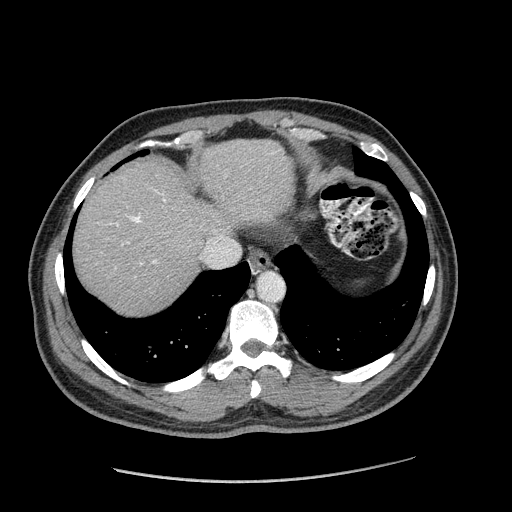
Contrast-enhanced abdominal CT (liver protocol), one axial slice. Slice 153 of 182 in the series (ordered by position). 120 kVp. Soft-tissue window (W 400 / L 40 HU). 512 × 512 image matrix. From the clinical record (not read from this slice): diagnosis: hepatocellular carcinoma (patient treated with transarterial chemoembolisation; whether this scan precedes or follows treatment is not stated here); TNM stage (as recorded): Stage-I.
Structures marked on this image (semi-automatic segmentation, software-assisted and operator-edited):
- abdominal aorta: bounding box <258,273,284,302> (left, top, right, bottom; pixels)
- liver parenchyma outside the tumour (the mass and vessels are separate outlines, so this box may not span the whole liver): <74,140,295,314>
- liver vessels: <116,190,165,263>